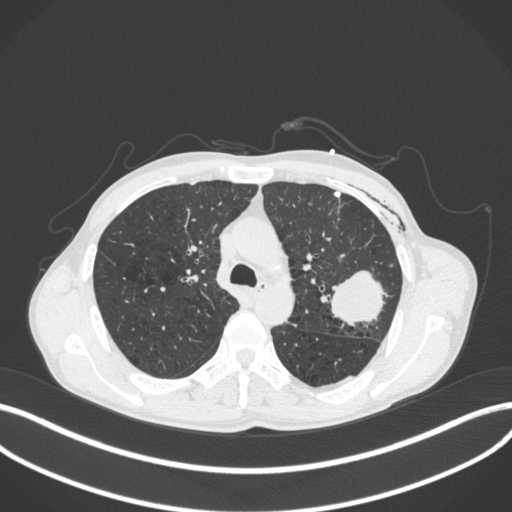
Chest CT, one axial slice; position 277 of 416 along the scan axis; reconstruction kernel B31f; lung window (W 1500 / L -600 HU); 1 mm slice thickness; 512 × 512 image matrix, field of view 400 × 400 mm. Male patient, age 58 years. From the clinical record (not read from this slice): clinical TNM (as recorded): T3 N0 M0.
Outlined on this slice (bounding box drawn by a radiologist):
- lung tumour (recorded histology: adenocarcinoma): bounding box (x1, y1, x2, y2) in pixels: (324, 262, 388, 327)